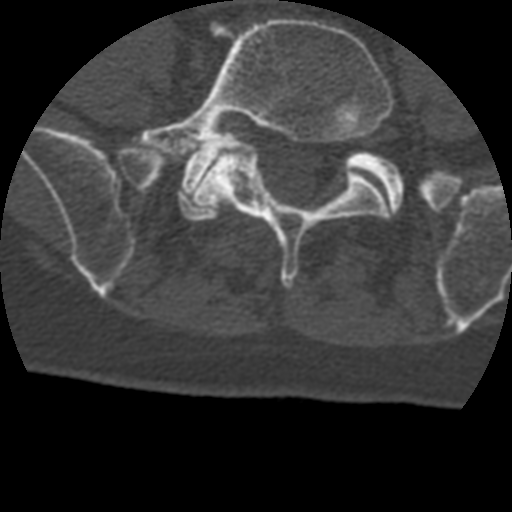
CT including the spine, one axial slice. Position 39 of 399 along the scan axis. Reconstruction kernel STANDARD. 120 kVp. Bone window (W 1800 / L 400 HU). 512 × 512 image matrix, field of view 160 × 160 mm. Patient age 69 years. From the clinical record (not read from this slice): primary cancer: prostate.
Outlined on this slice (semi-automatically segmented with operator editing):
- L5 vertebra: box from (x=132, y=18) to (x=393, y=289) px